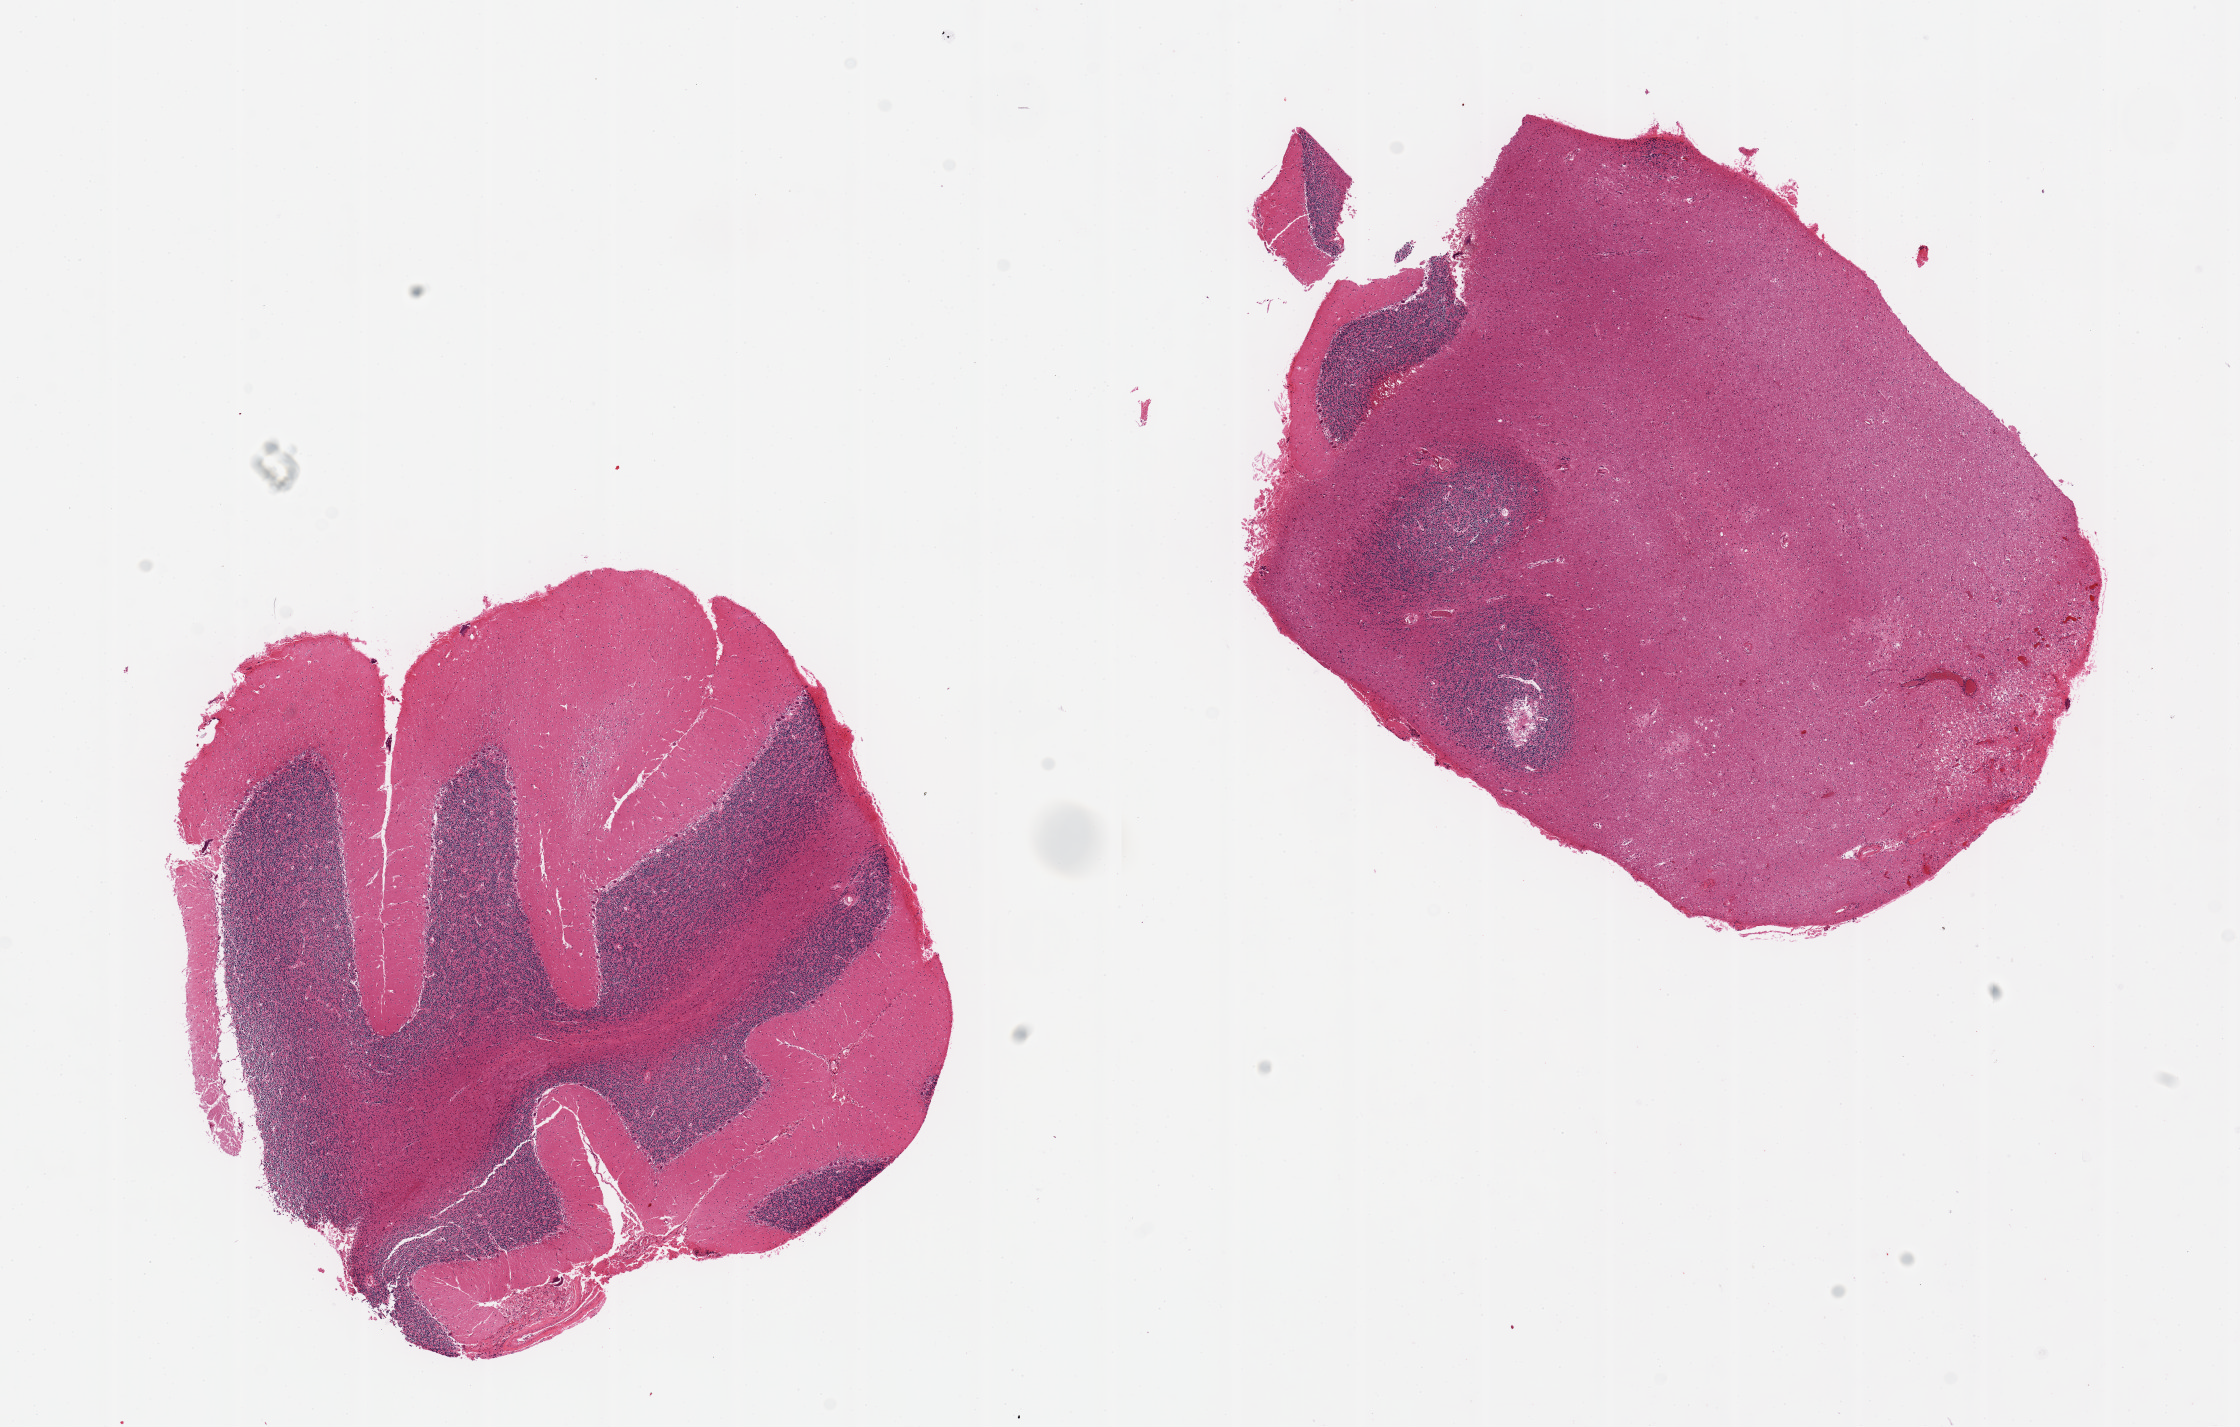
Digitized hematoxylin and eosin (H&E)-stained section, a low-resolution overview of the entire scanned area, about 17.7 x 11.3 mm. PAXgene-fixed, paraffin-embedded tissue. Target tissue: cerebellum. Tissue donor sample. Donor sex: male.
Review note (as recorded): Well-preserved.